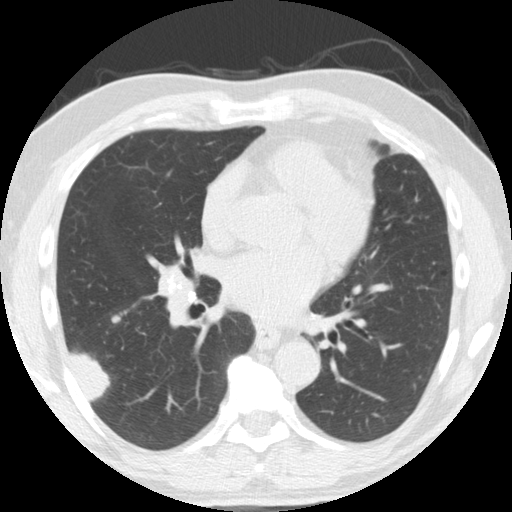
Chest CT (low-dose screening protocol), one axial image; second screening round (one year after baseline); lung window (W 1500 / L -600 HU); 2.5 mm slice thickness; slice 93 of 174 in the series; 512 × 512 image matrix. Male participant, aged 61 years at enrolment. Former smoker at enrolment.
Lesion marked by an expert reader, box from (x=51, y=327) to (x=118, y=402) px. Reader record for this screening exam (exam-level; its link to the box is not recorded): non-calcified nodule or mass ≥4 mm, right lower lobe, 33 × 19 mm, smooth margins, soft tissue attenuation, pre-existing on the prior screen: yes; interval growth: yes. Participant outcome: lung cancer diagnosed 30 days after this screen — adenosquamous carcinoma, right lower lobe, poorly differentiated (G3), stage IV (AJCC 6th edition), 45 mm at pathology.